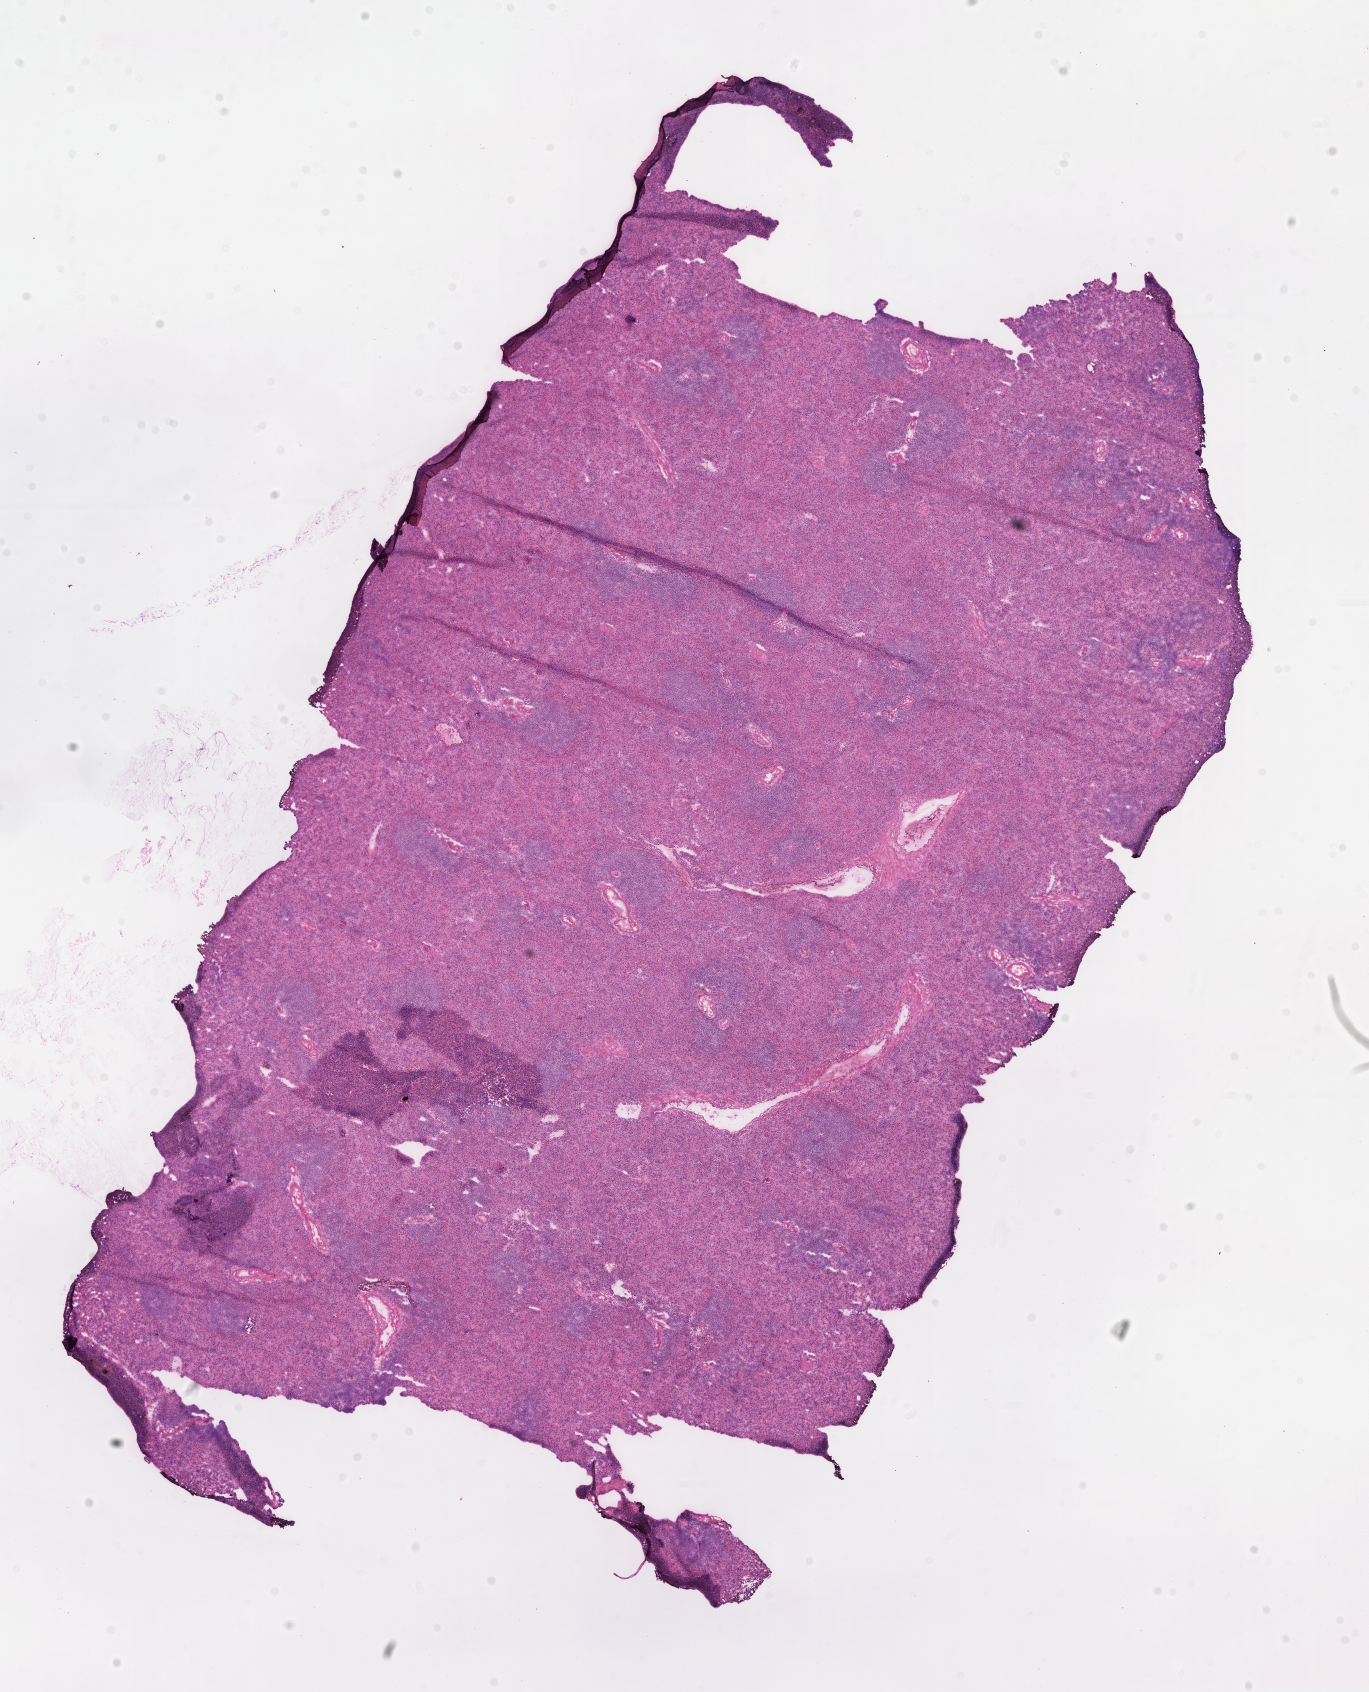
Whole-slide image, haematoxylin and eosin stain, shown as a low-resolution overview of the whole scanned area (about 11.1 x 13.7 mm), frozen section, specimen: normal-tissue sample (non-tumor) from a patient with intraductal papillary mucinous neoplasm with invasive carcinoma, site: head of pancreas. Male, age 77 years at initial diagnosis. Composition of this section per pathologist review: tumor cells 0%, tumor nuclei 0%, stromal cells 0%, necrosis 0%, normal cells 100%. Inflammatory infiltration, as recorded: lymphocyte infiltration 0%, monocyte infiltration 0%, neutrophil infiltration 0%.
This section: non-tumor tissue sample; the patient's diagnosis is given above. Section: bottom of the tissue portion.